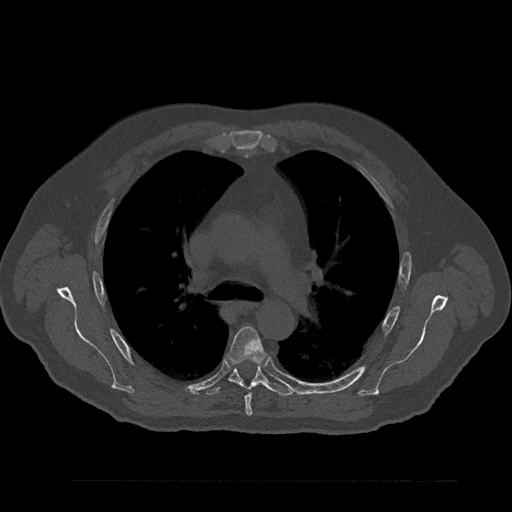
CT including the spine, one axial slice; slice 581 of 797 in the series (ordered by position); 120 kVp; bone window (W 1800 / L 400 HU); 512 × 512 image matrix. Male patient, age 61 years. From the clinical record (not read from this slice): primary cancer: prostate.
Outlined on this slice (semi-automatic segmentation, software-assisted and operator-edited):
- T5 vertebra: bounding box <228,326,266,416> (left, top, right, bottom; pixels)
- T6 vertebra: <205,363,293,397>